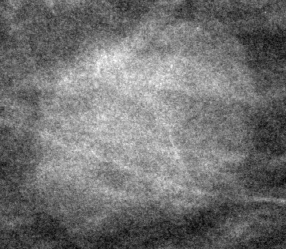
Cropped region of a digitized screen-film mammogram centred on a radiologist-marked abnormality, right breast, CC view, BI-RADS breast density category 2 (scale 1–4).
Marked abnormality: mass, shape oval, margins circumscribed; BI-RADS assessment category 3; subtlety rating 5 on a 1 (subtle) to 5 (obvious) scale; pathology result (as recorded, not read from the image): benign.